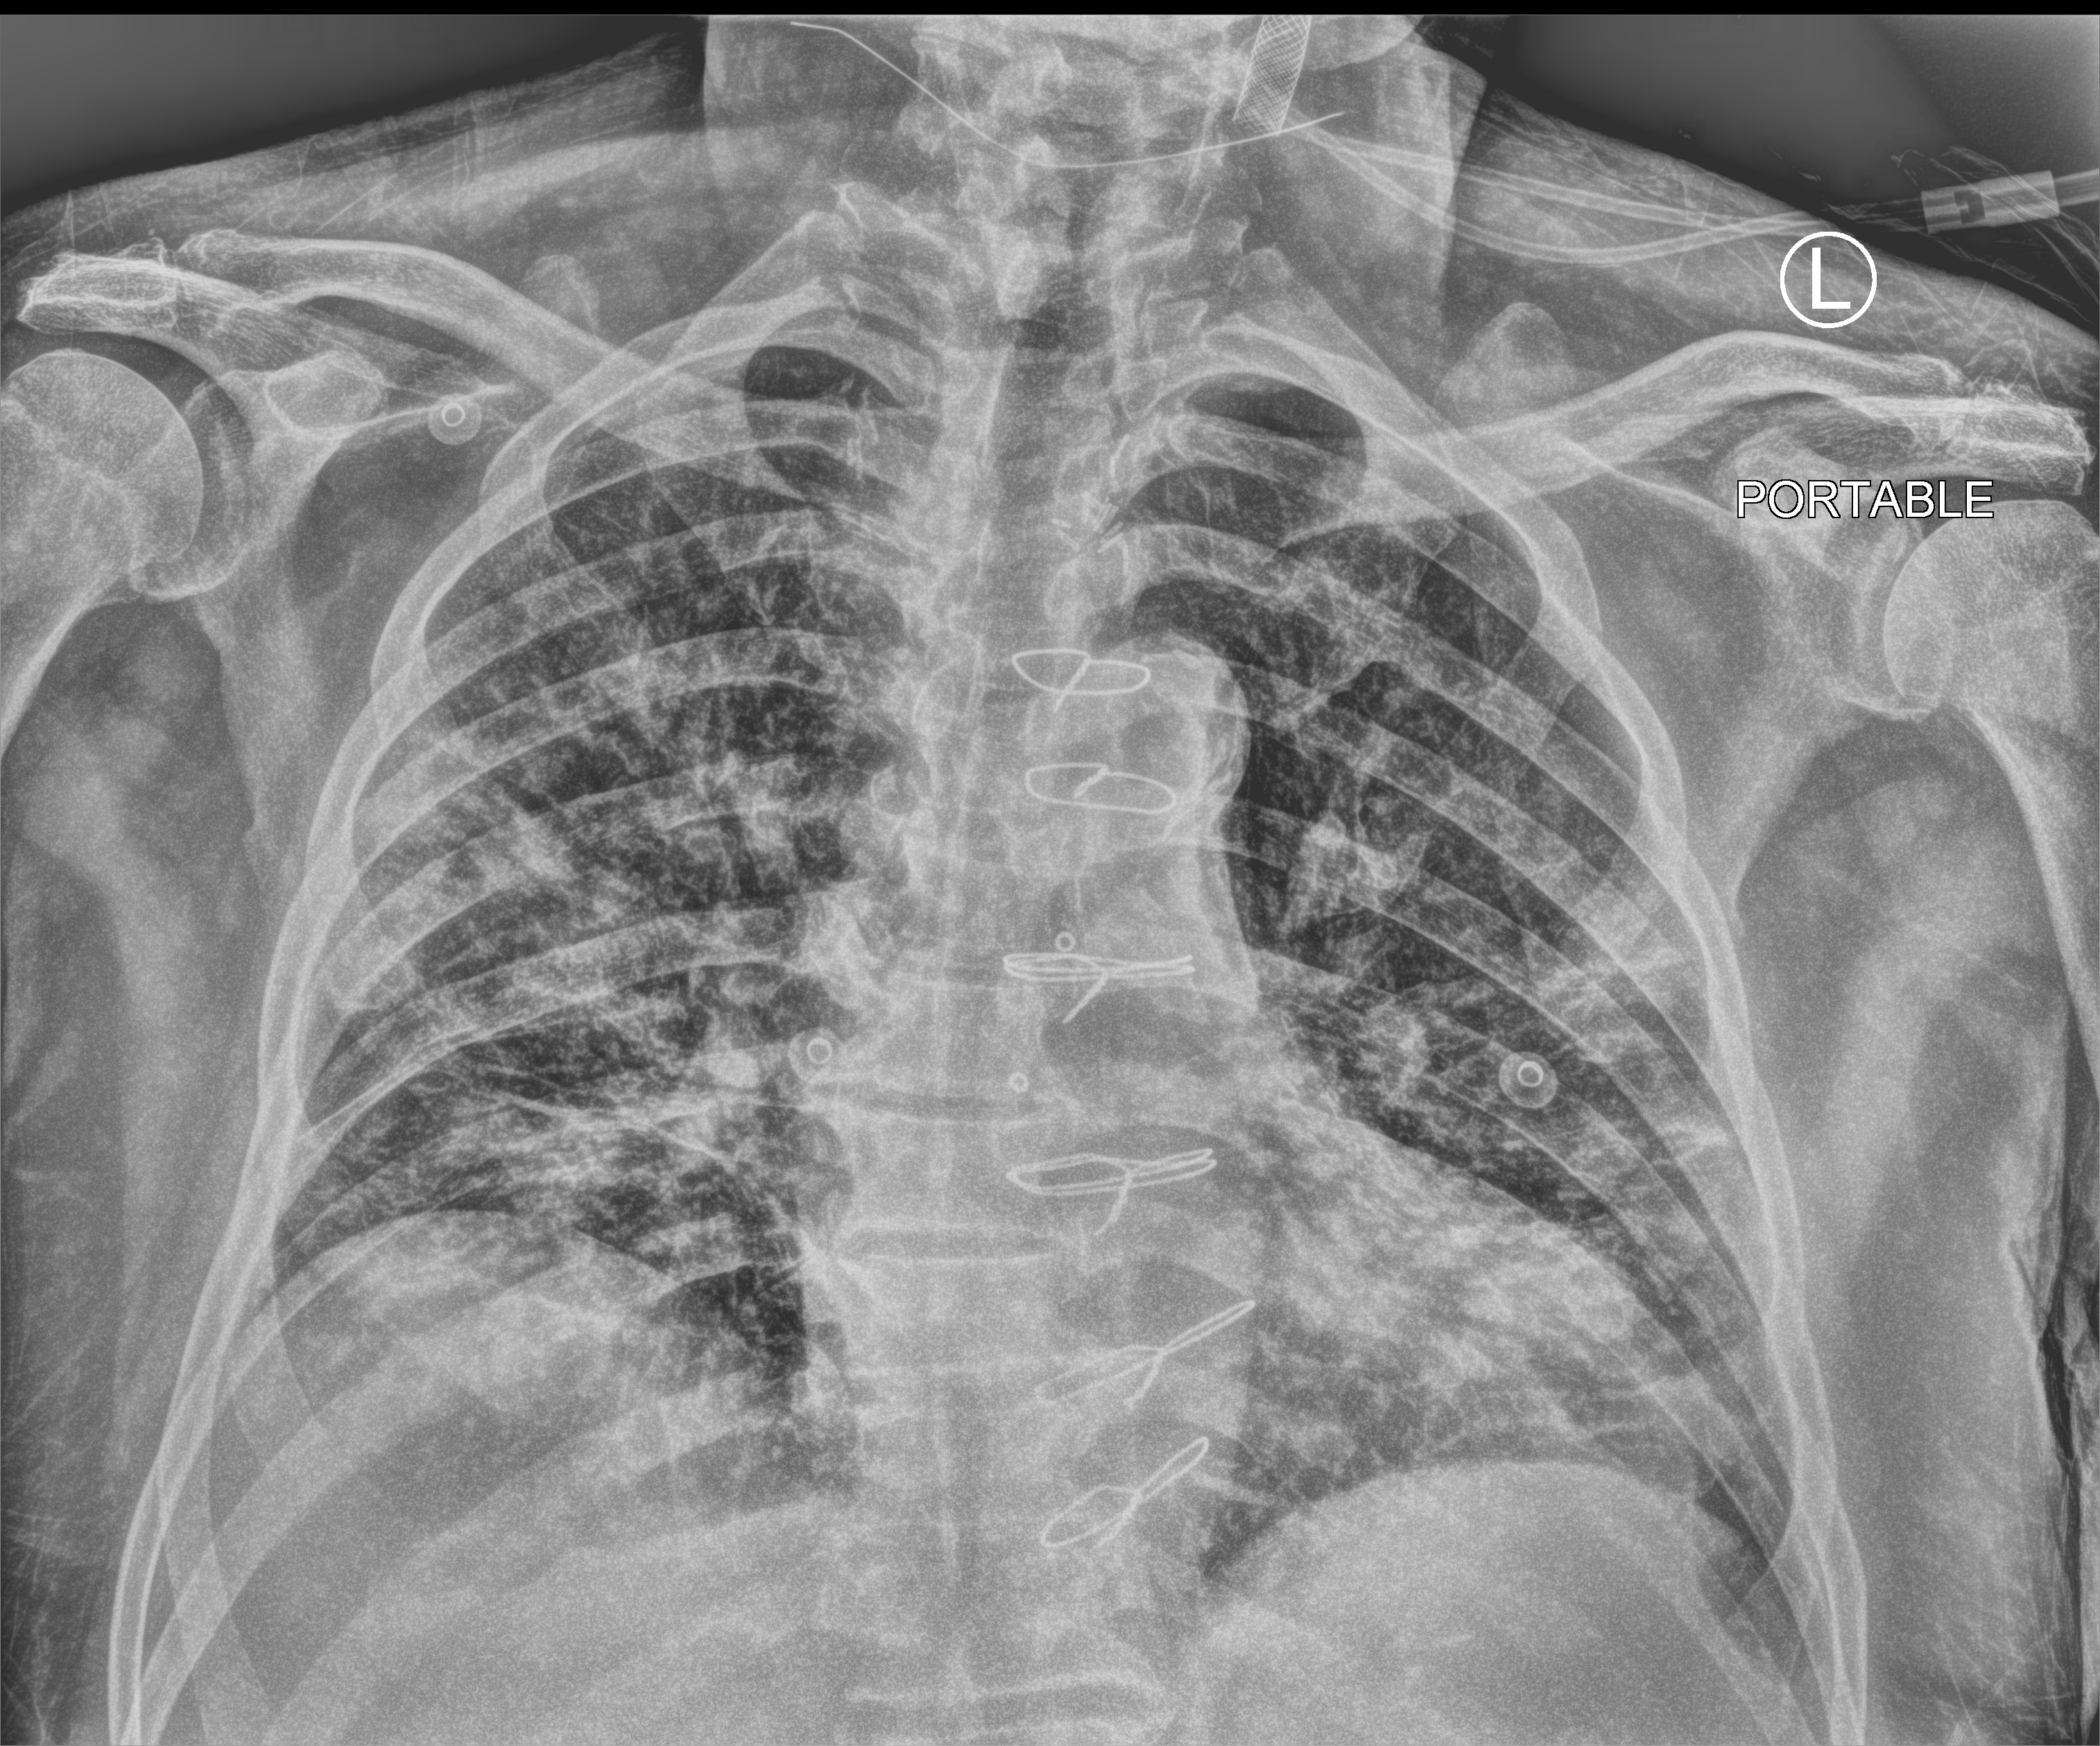
Chest X-ray (portable). Patient hospitalised with COVID-19; male, aged 75–90 years.
From the hospital-stay record, not from the radiograph (when in the stay this image was taken is not recorded): mechanically ventilated during this hospital stay: no.